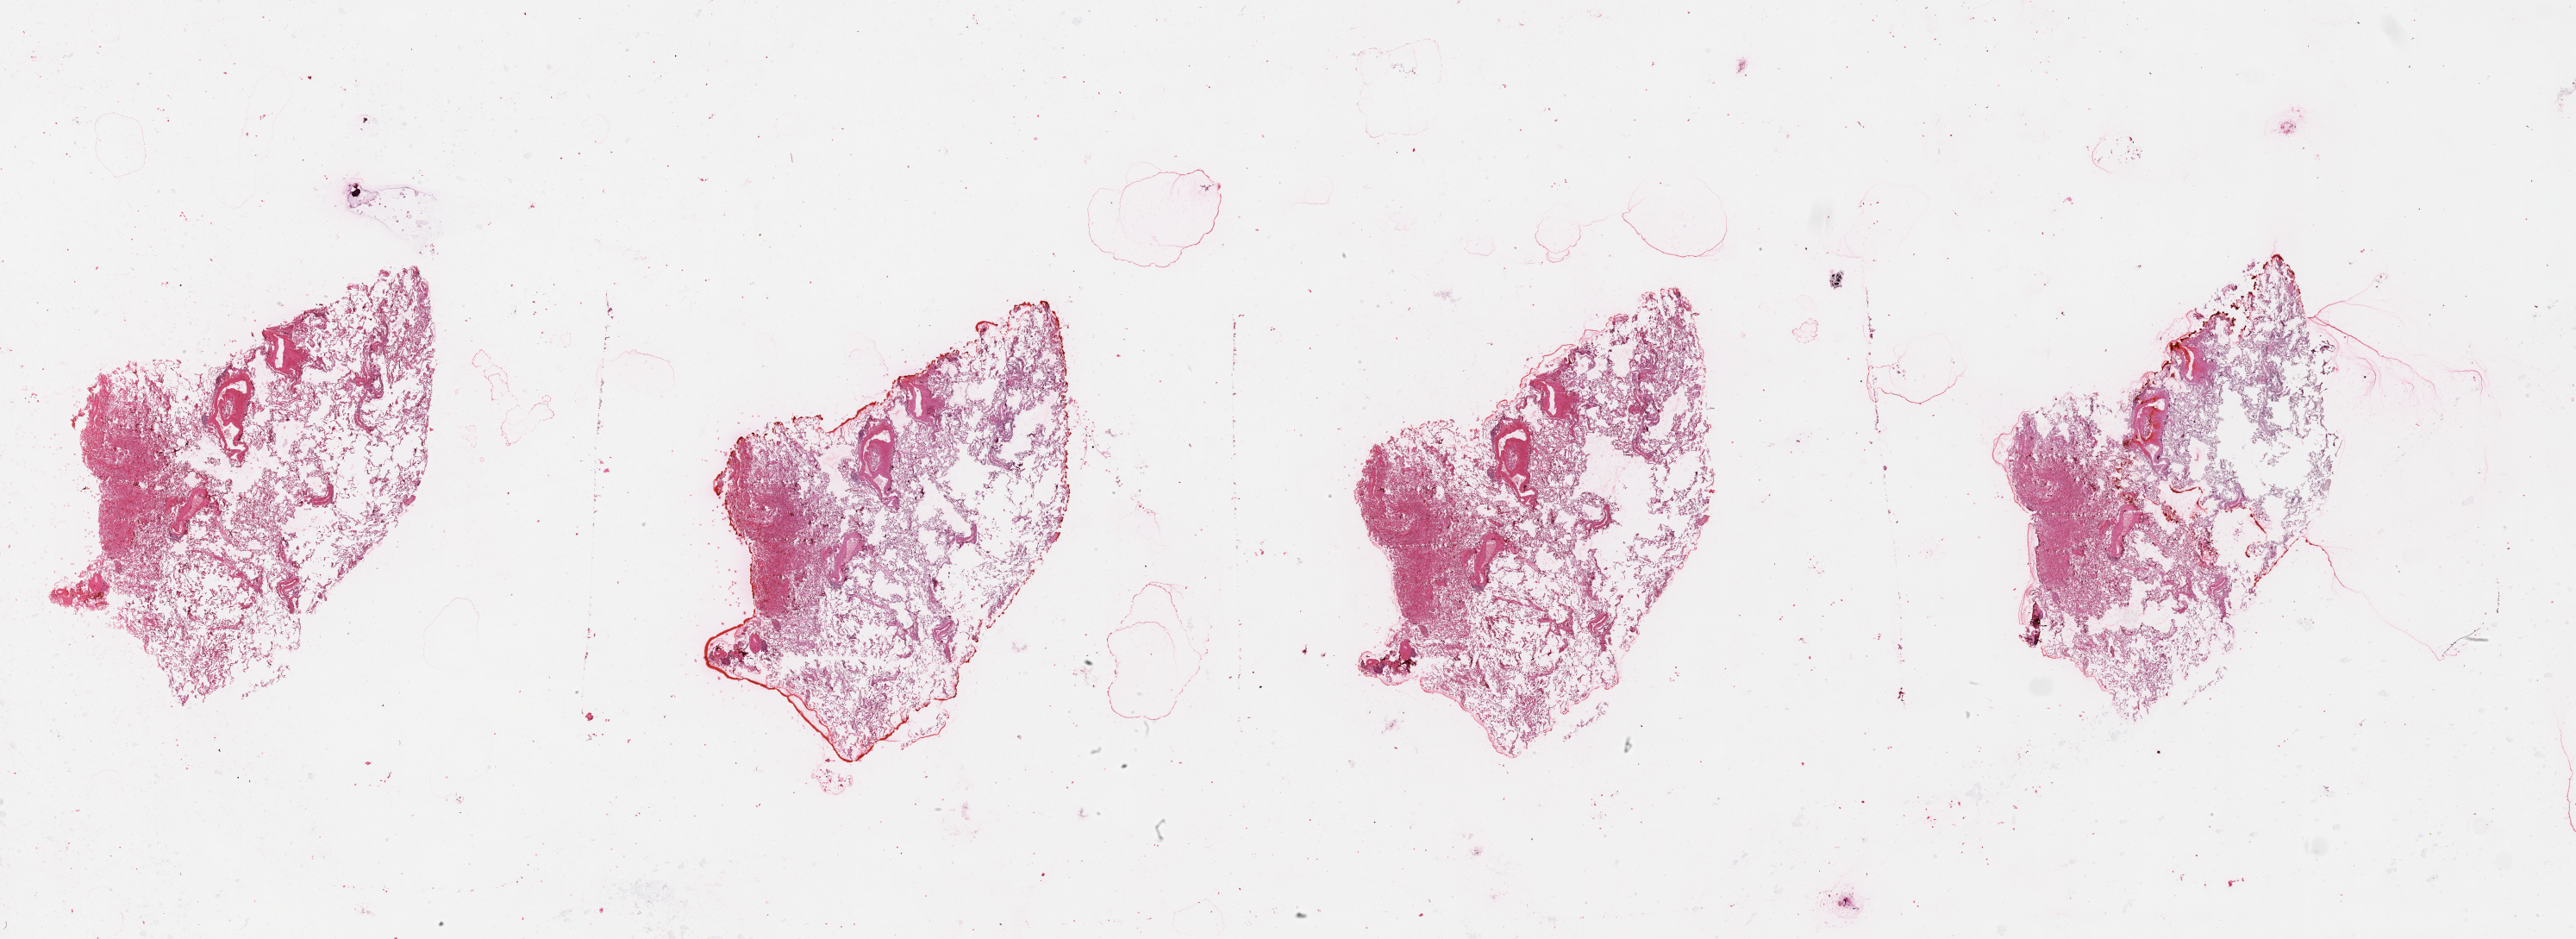
Digitized Hematoxylin and eosin (H&E) stained tissue section (whole slide), shown as a low-resolution overview of the whole scanned area (about 48.1 x 17.5 mm). Lung, tissue type not recorded.
Patient diagnosis (cohort enrolment): squamous cell carcinoma (lung).